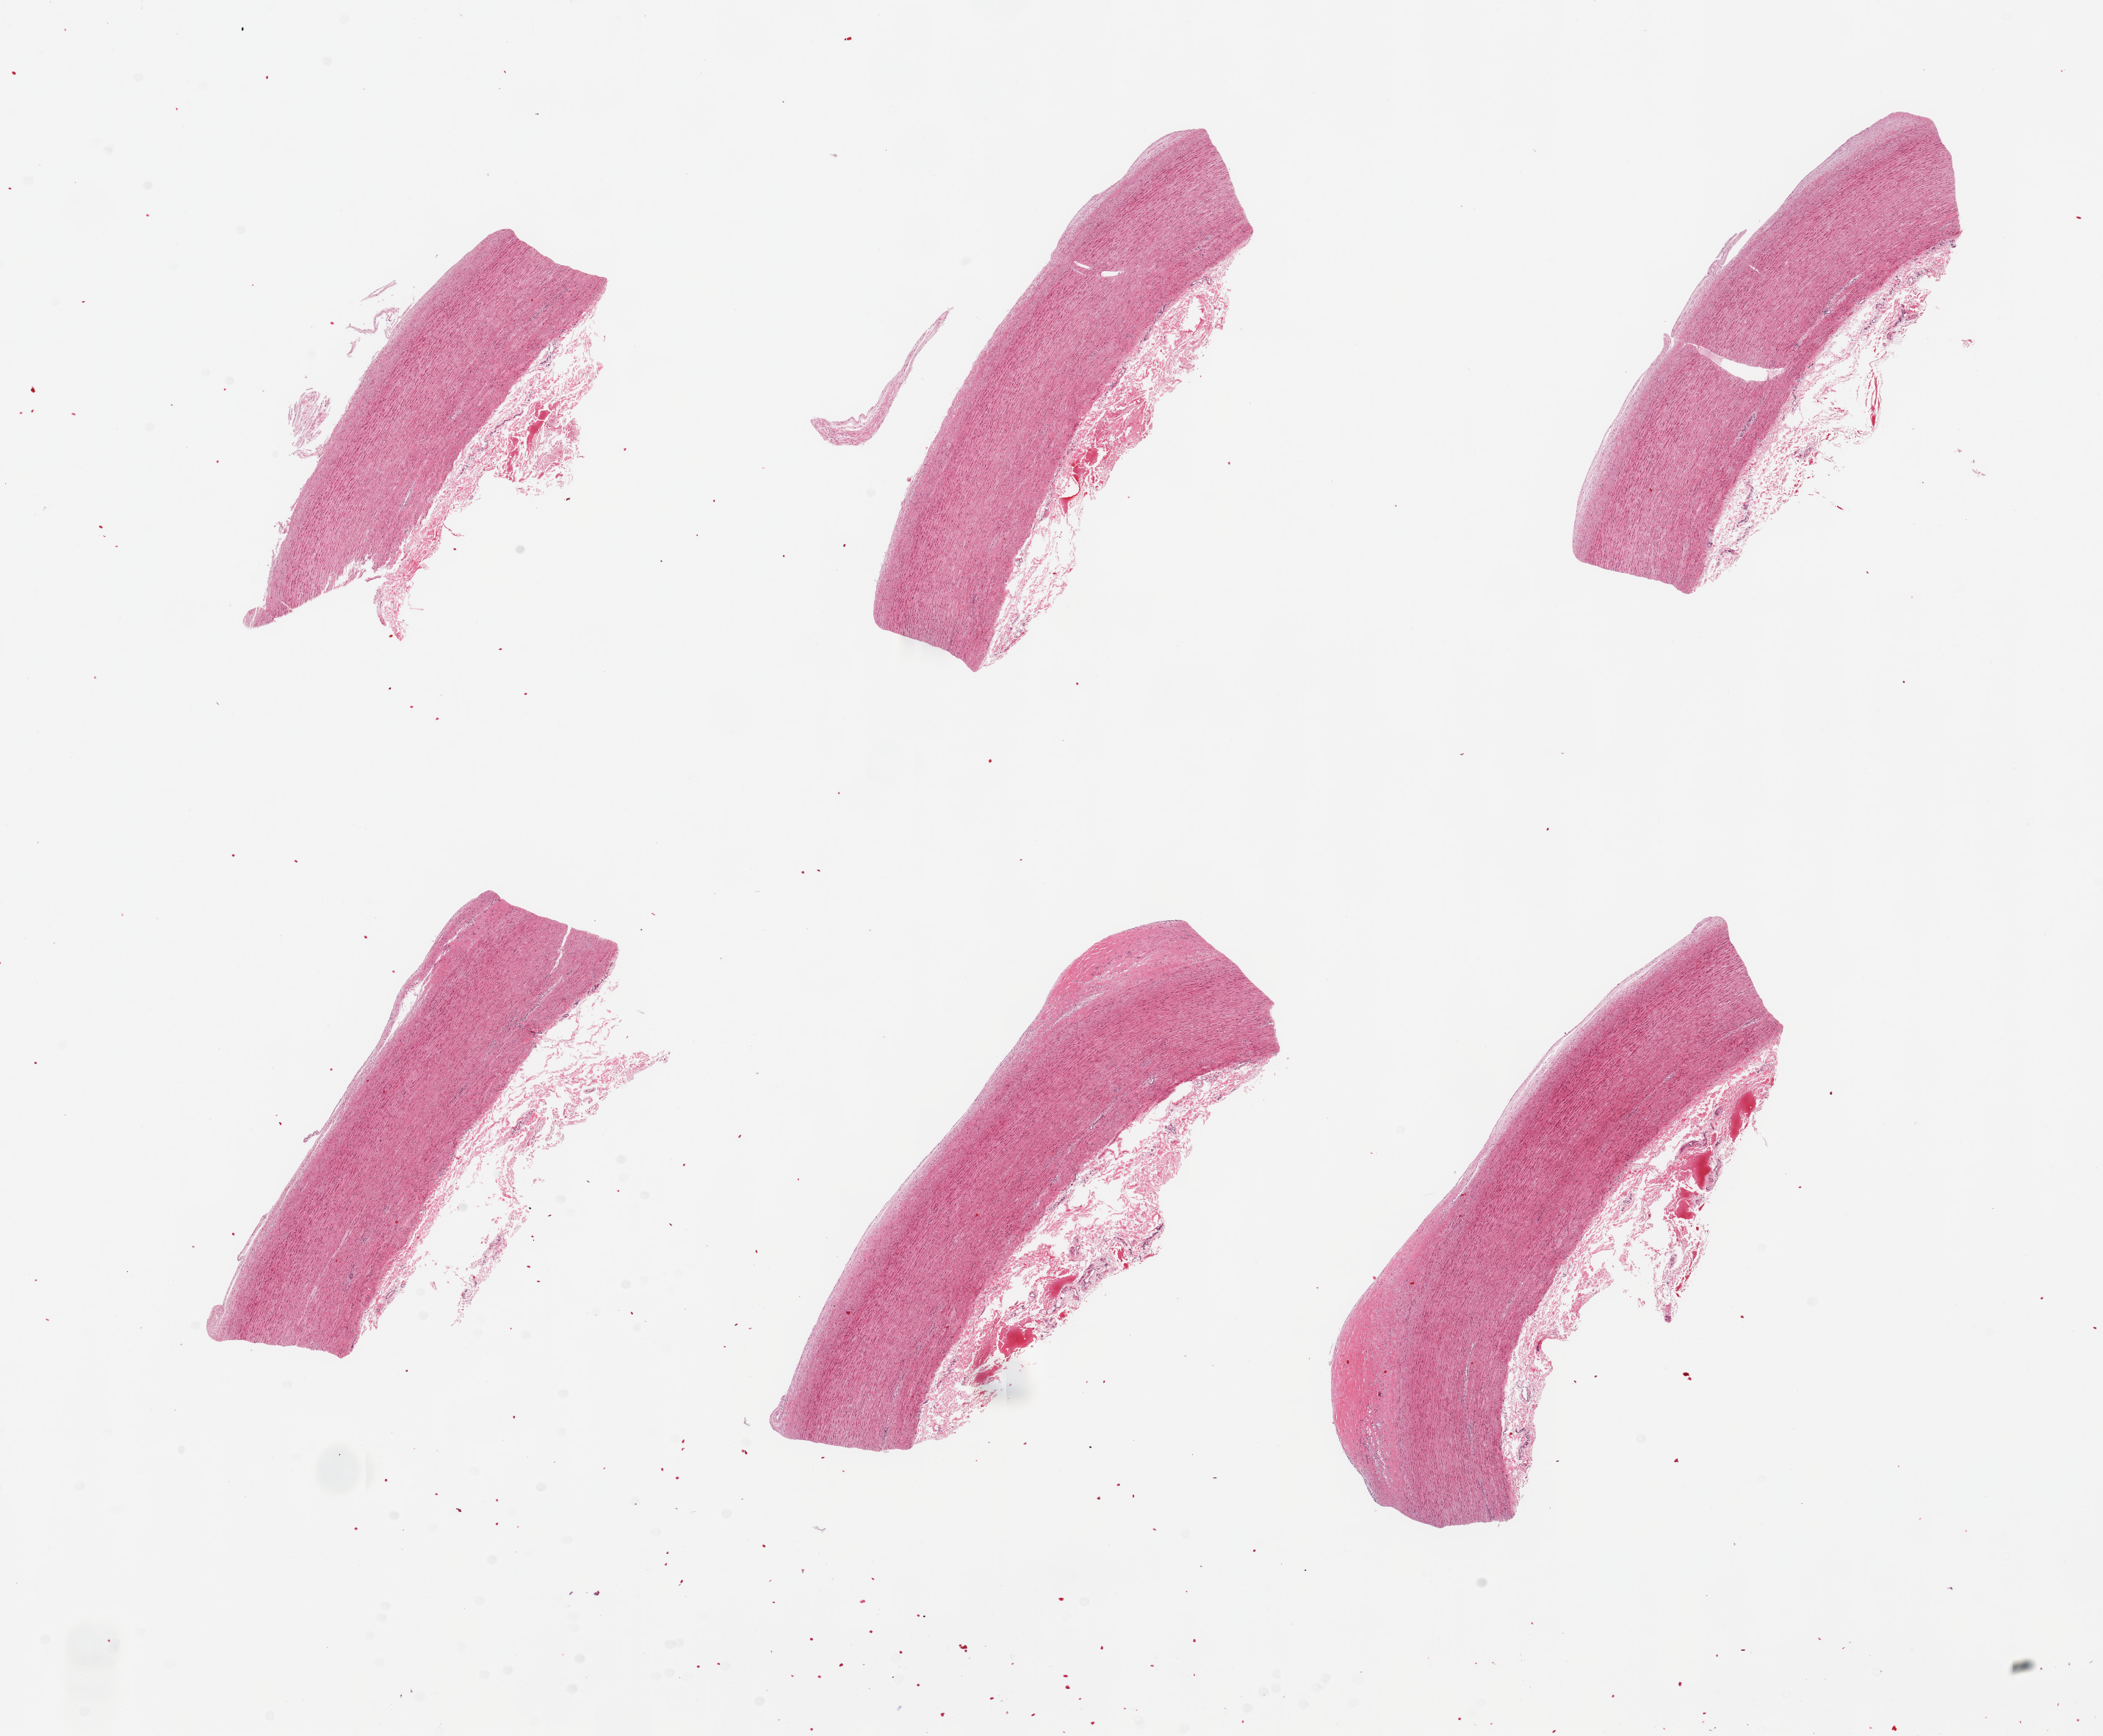
Whole-slide image, H&E stain, a low-resolution overview of the entire scanned area, about 22.6 x 18.7 mm. PAXgene-fixed, paraffin-embedded tissue. Target tissue: aorta. Tissue donor sample. Donor: male.
- review note (as recorded): 6 pieces; some atherosclerosis